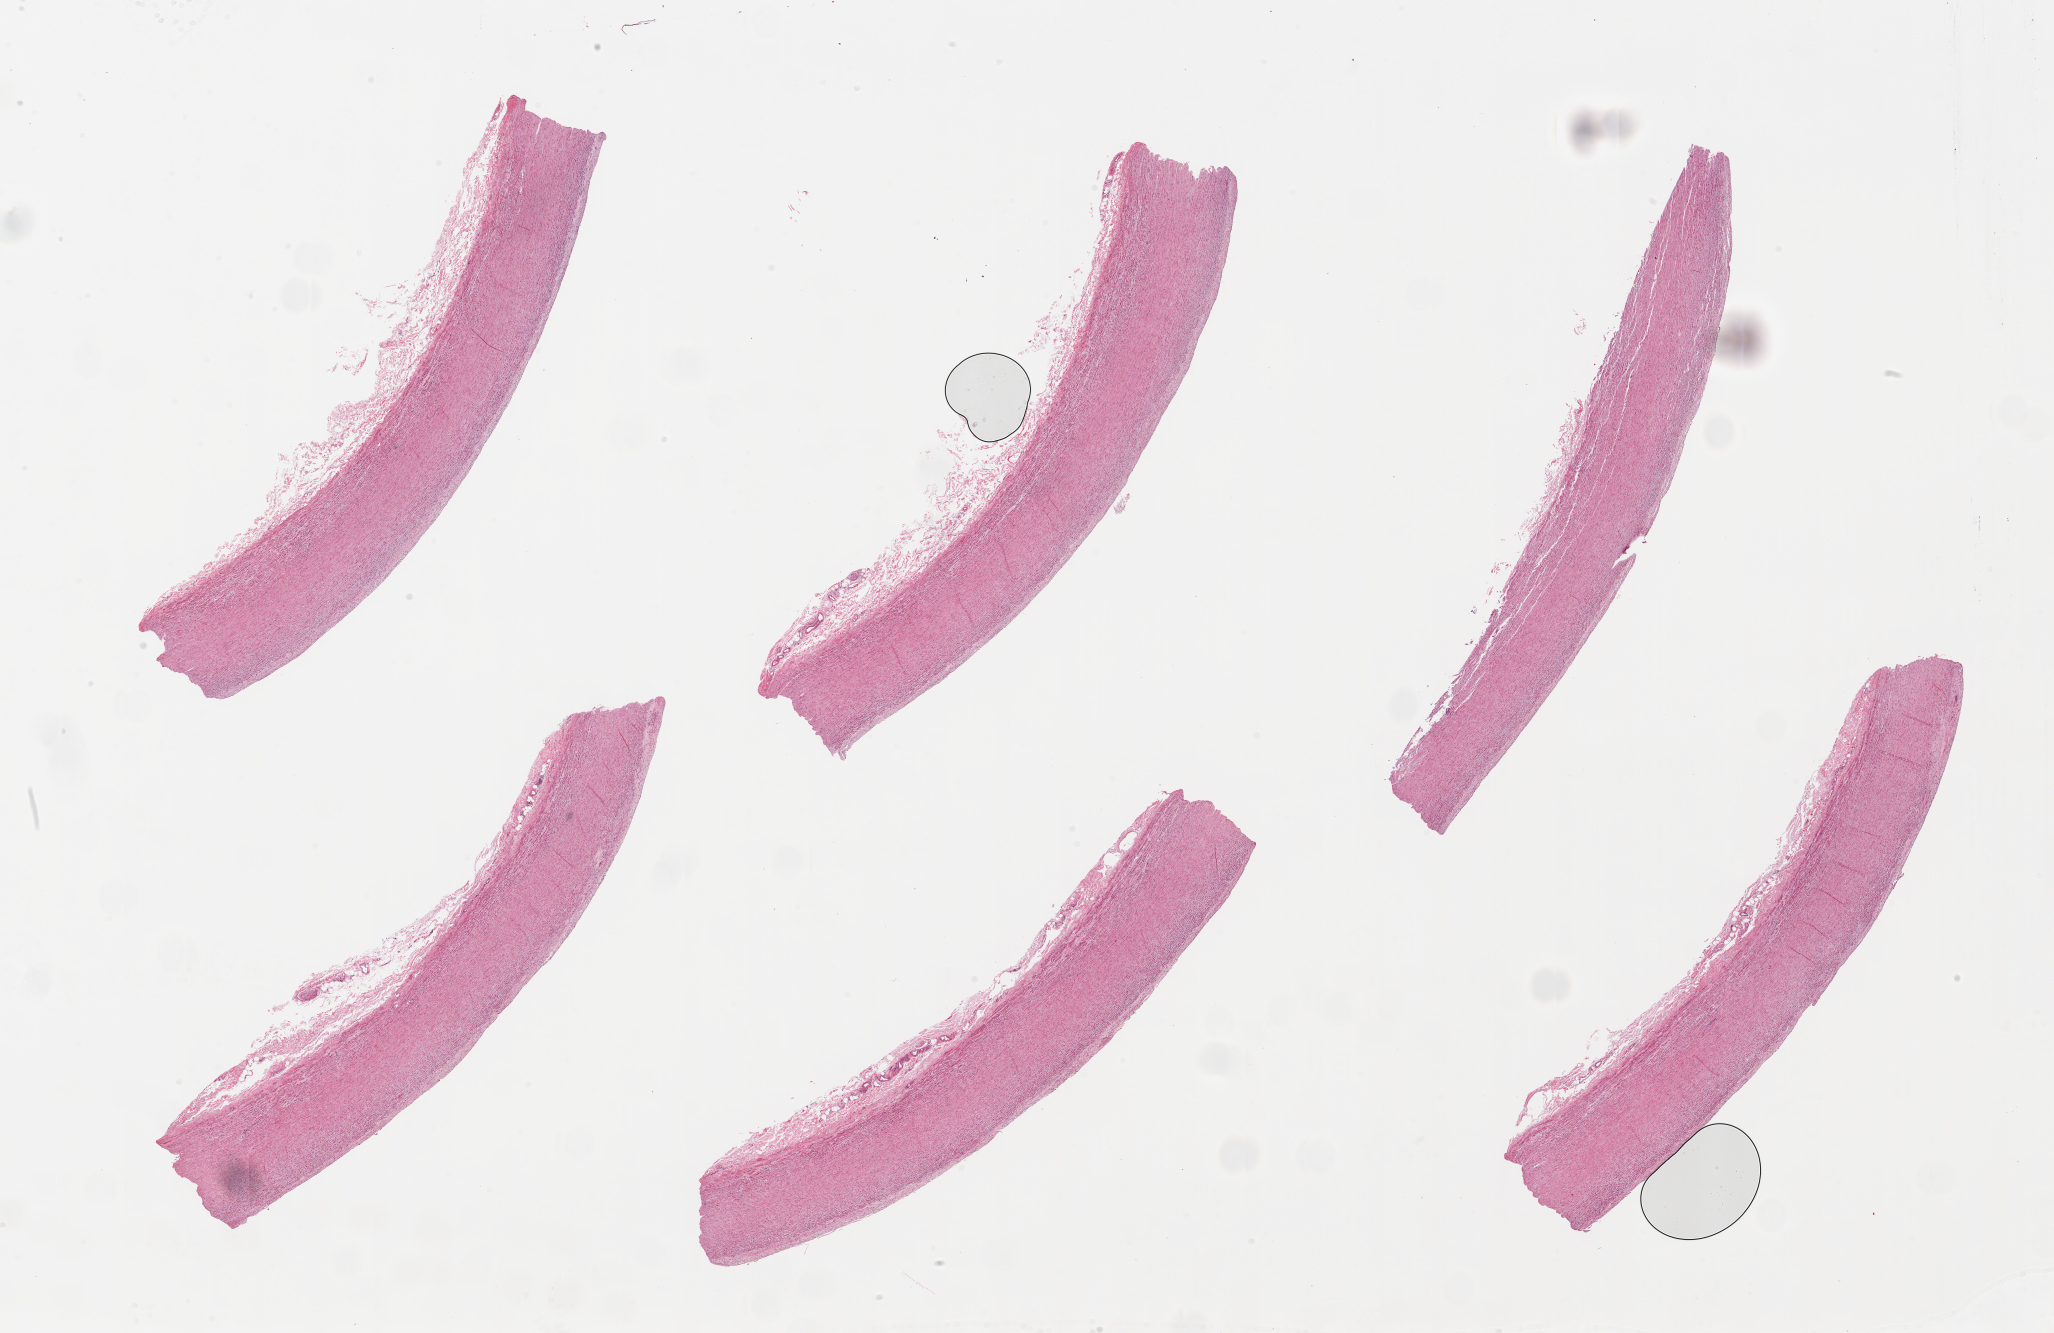
Whole-slide image, haematoxylin and eosin stain, brightfield, whole scanned area (about 32.5 x 21.1 mm) shown as a low-resolution overview. PAXgene-fixed paraffin-embedded (PFPE) section. Section of aorta (target tissue). Donor tissue sample. Donor: female.
* review note (as recorded): 6 pieces, up to 11x2mm; up to ~1mm adeherent serosa/vasa vasorum